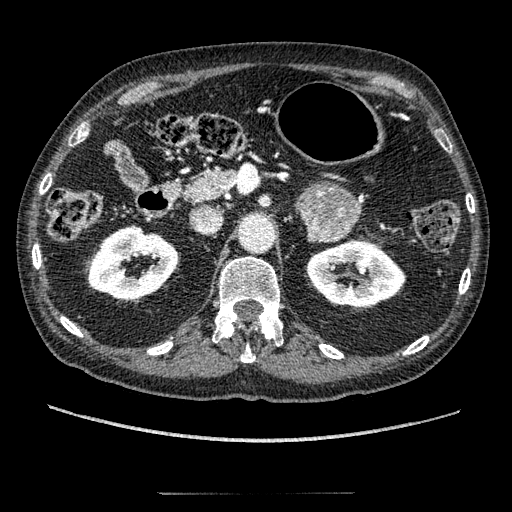
Contrast-enhanced abdominal CT, one axial slice; slice 119 of 274 in the series (ordered by position); reconstruction kernel STANDARD; soft-tissue window (W 400 / L 40 HU); 1.25 mm slice thickness; 512 × 512 image matrix, field of view 381 × 381 mm. Patient: male, 69 years. Case-level facts recorded for this patient, not image findings: diagnosis: adrenocortical carcinoma; tumour side: left adrenal; tumour size at pathology: 6.1 cm; Ki-67 index: 10 %; stage (as recorded): 3.
Structures marked on this image (semi-automatically segmented with operator editing):
- mass: box from (x=298, y=184) to (x=360, y=241) px